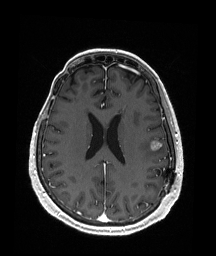
Brain MRI from a brain-tumour surgery series, one axial slice; slice 76 of 176 in the series (ordered by position); T1-weighted post-contrast; 1 mm slice thickness; 216 × 256 image matrix, field of view 211 × 250 mm. Case-level facts recorded for this patient, not image findings: histopathology: Metastatic Malignant Melanoma.
Structures marked on this image (outlined manually by an expert reader):
- tumour: bounding box <150,140,162,150> (left, top, right, bottom; pixels)